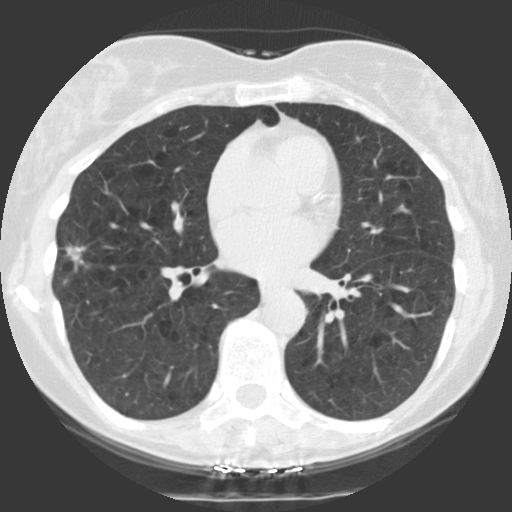
Chest CT (low-dose screening protocol), one axial image, first (baseline) screen, lung window (W 1500 / L -600 HU), 2.5 mm slice thickness. Female participant, aged 68 years at enrolment. Former smoker at enrolment.
Expert-annotated lung lesion, box from (x=50, y=234) to (x=104, y=286) px. The screening reader recorded 2 non-calcified nodules or masses ≥4 mm on this exam (right lower lobe, right middle lobe); which of them this box marks is not recorded. Official screen result: positive, change unspecified: nodule(s) >= 4 mm or enlarging nodule(s), mass(es), or other non-specific abnormalities suspicious for lung cancer. Participant outcome: lung cancer diagnosed 40 days after this screen — bronchiolo-alveolar adenocarcinoma, NOS, right upper lobe, right middle lobe, right lower lobe, well differentiated (G1), stage IV (AJCC 6th edition).